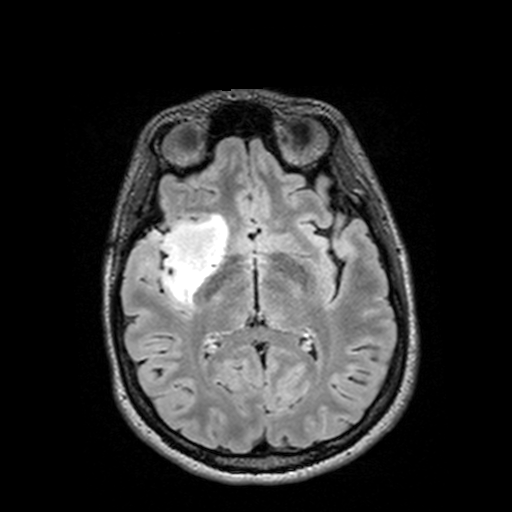
Brain MRI from a brain-tumour surgery series, one axial slice. Slice 73 of 144 in the series (ordered by position). T2 FLAIR. 1 mm slice thickness. 512 × 512 image matrix, field of view 250 × 250 mm. From the clinical record (not read from this slice): histopathology: Astrocytoma; WHO grade: 3; IDH mutation: yes.
Annotated regions visible in this slice (expert manual segmentation):
- tumour: box from (x=126, y=213) to (x=232, y=302) px